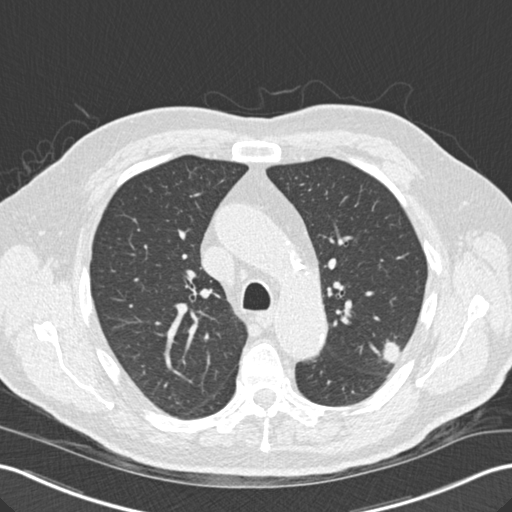
Low-dose screening chest CT, axial slice; third screening round (two years after baseline); lung window (W 1500 / L -600 HU); standard (soft-tissue) reconstruction kernel (B30f); 512 × 512 image matrix, field of view 354 × 354 mm. Male, age 67 years at enrolment. Former smoker at enrolment.
Lesion marked by an expert reader, bounding box <365,332,411,374> (left, top, right, bottom; pixels). The screening reader recorded 2 non-calcified nodules or masses ≥4 mm on this exam; which of them this box marks is not recorded.